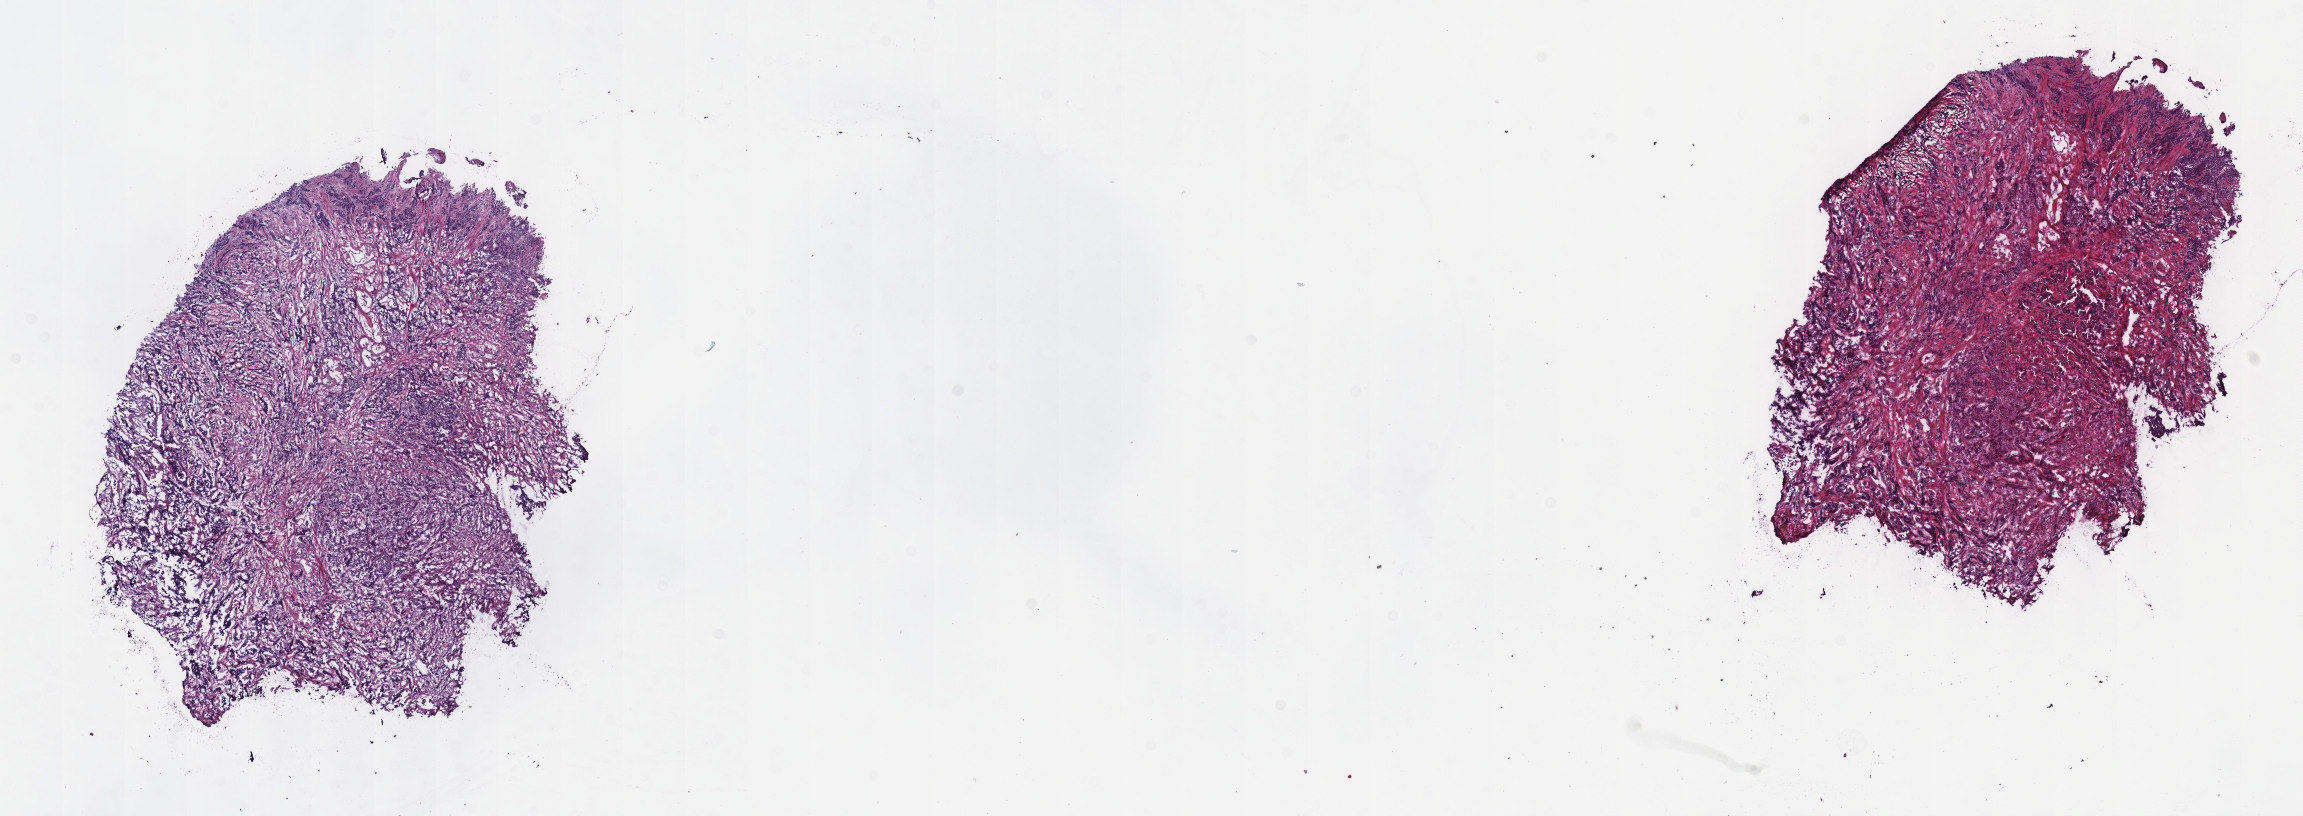
Whole-slide histology image, H&E-stained, shown as a low-resolution overview of the whole scanned area (about 18.6 x 6.6 mm, slide scanned at 40x), frozen section from the top of the tissue portion, primary tumour sample from the prostate. Patient: male, age at initial diagnosis 66 years. Gleason score: 9 (4+5). Slide review estimates, as recorded: tumour cells 75%, tumour nuclei 85%, normal cells 0%, stromal cells 25%, necrosis 0%. Infiltration values recorded for this section: lymphocyte infiltration 0%, monocyte infiltration 0%, neutrophil infiltration 0%.
Diagnosis: Adenocarcinoma, NOS (prostate gland).